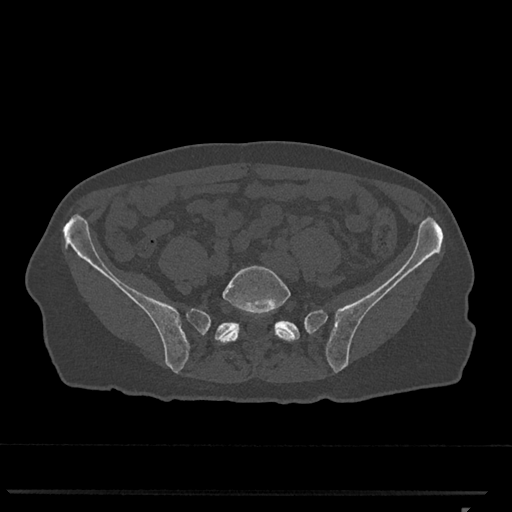
CT including the spine, one axial slice. Reconstruction kernel Br40s/3. 120 kVp. Bone window (W 1800 / L 400 HU). 0.5 mm slice thickness. 512 × 512 image matrix, field of view 380 × 380 mm. Patient: female, 62 years. Case-level facts recorded for this patient, not image findings: primary cancer: renal.
Outlined on this slice (semi-automatically segmented with operator editing):
- L5 vertebra: bounding box (x1, y1, x2, y2) in pixels: (219, 265, 297, 345)